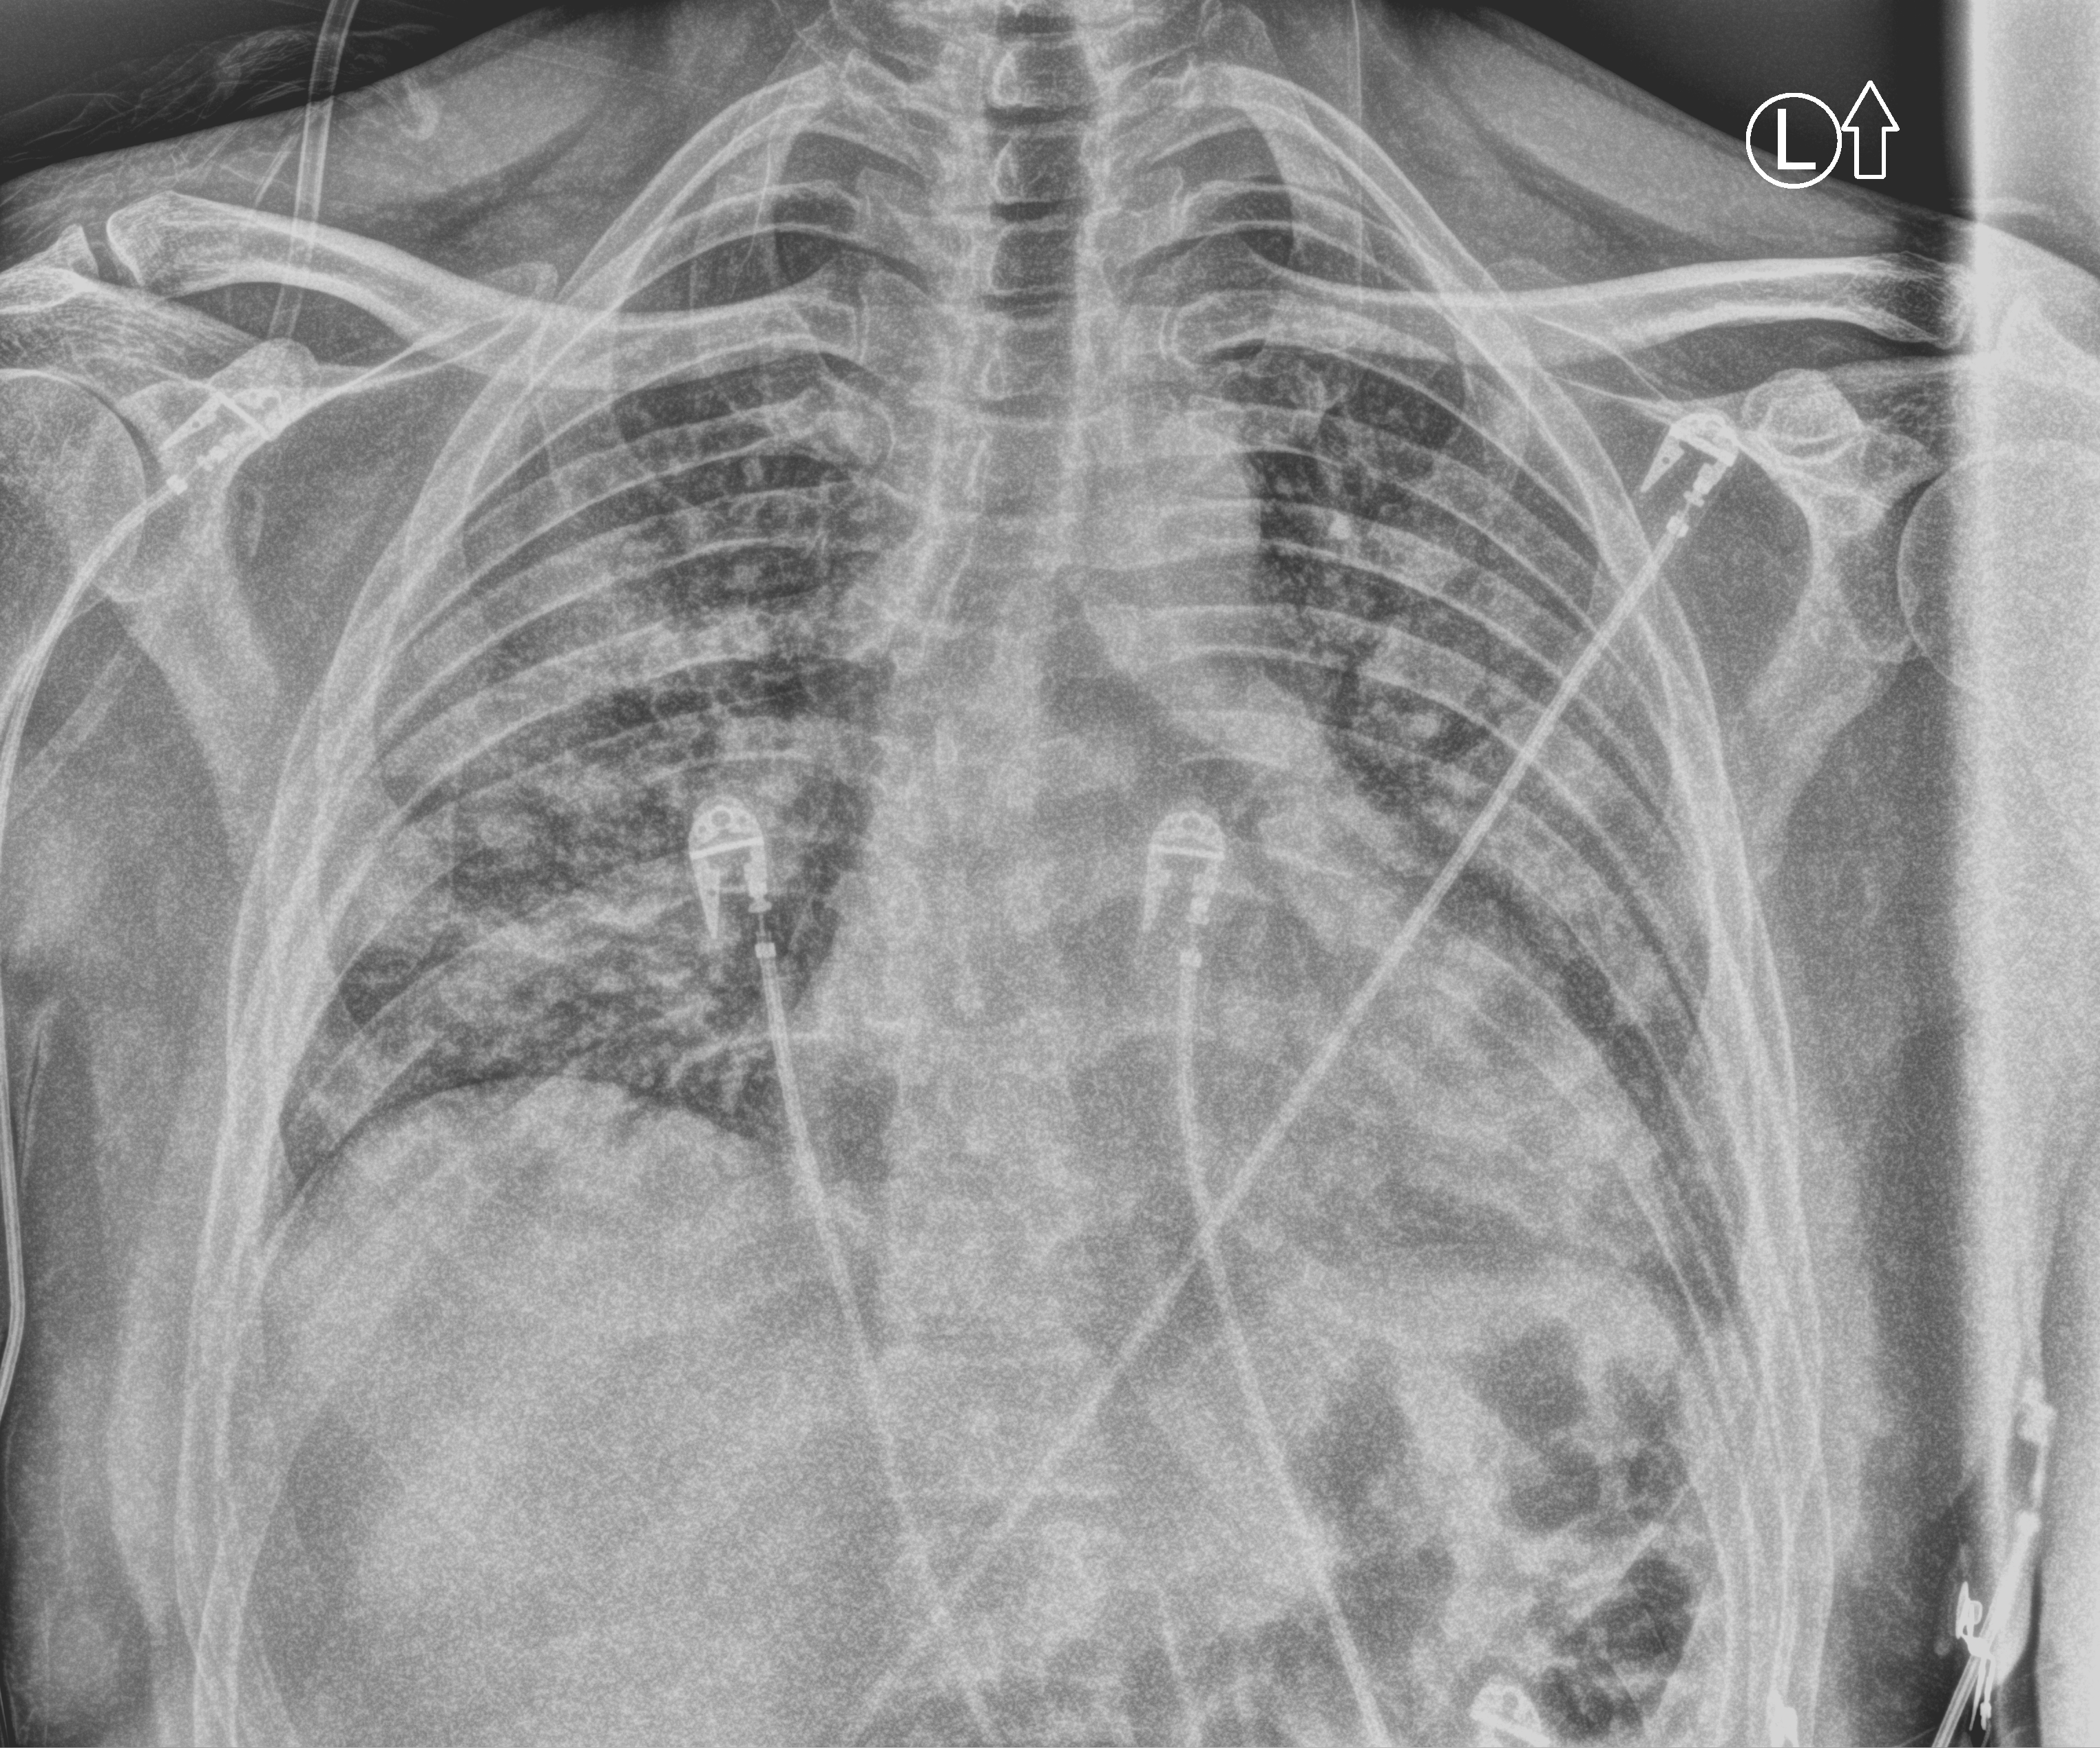
Chest X-ray (portable). Male patient hospitalised with COVID-19, age 18–59 years.
Admission-level facts for this patient (not findings on this image; timing relative to this image not recorded): COPD (admission record): no.